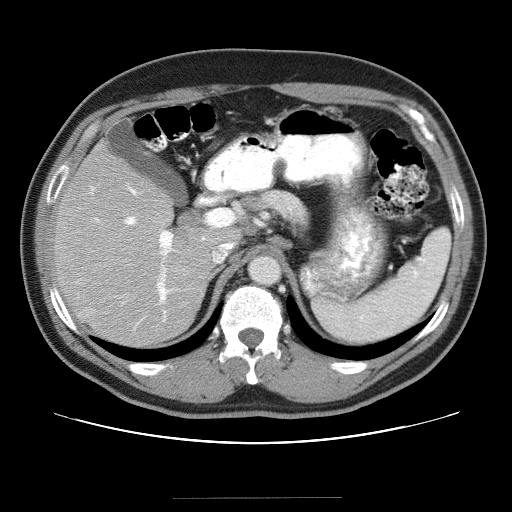
Contrast-enhanced abdominal CT (liver protocol), one axial slice; position 21 of 40 along the scan axis; reconstruction kernel STANDARD; soft-tissue window (W 400 / L 40 HU); 5 mm slice thickness; 512 × 512 image matrix. Case-level facts recorded for this patient, not image findings: diagnosis: hepatocellular carcinoma (patient treated with transarterial chemoembolisation; whether this scan precedes or follows treatment is not stated here); TNM stage (as recorded): Stage-IVA; Child-Pugh class: B; tumour nodularity: multinodular.
Annotated regions visible in this slice (semi-automatically segmented with operator editing):
- liver parenchyma outside the tumour (the mass and vessels are separate outlines, so this box may not span the whole liver): bounding box (x1, y1, x2, y2) in pixels: (54, 140, 242, 346)
- liver vessels: (91, 187, 206, 325)